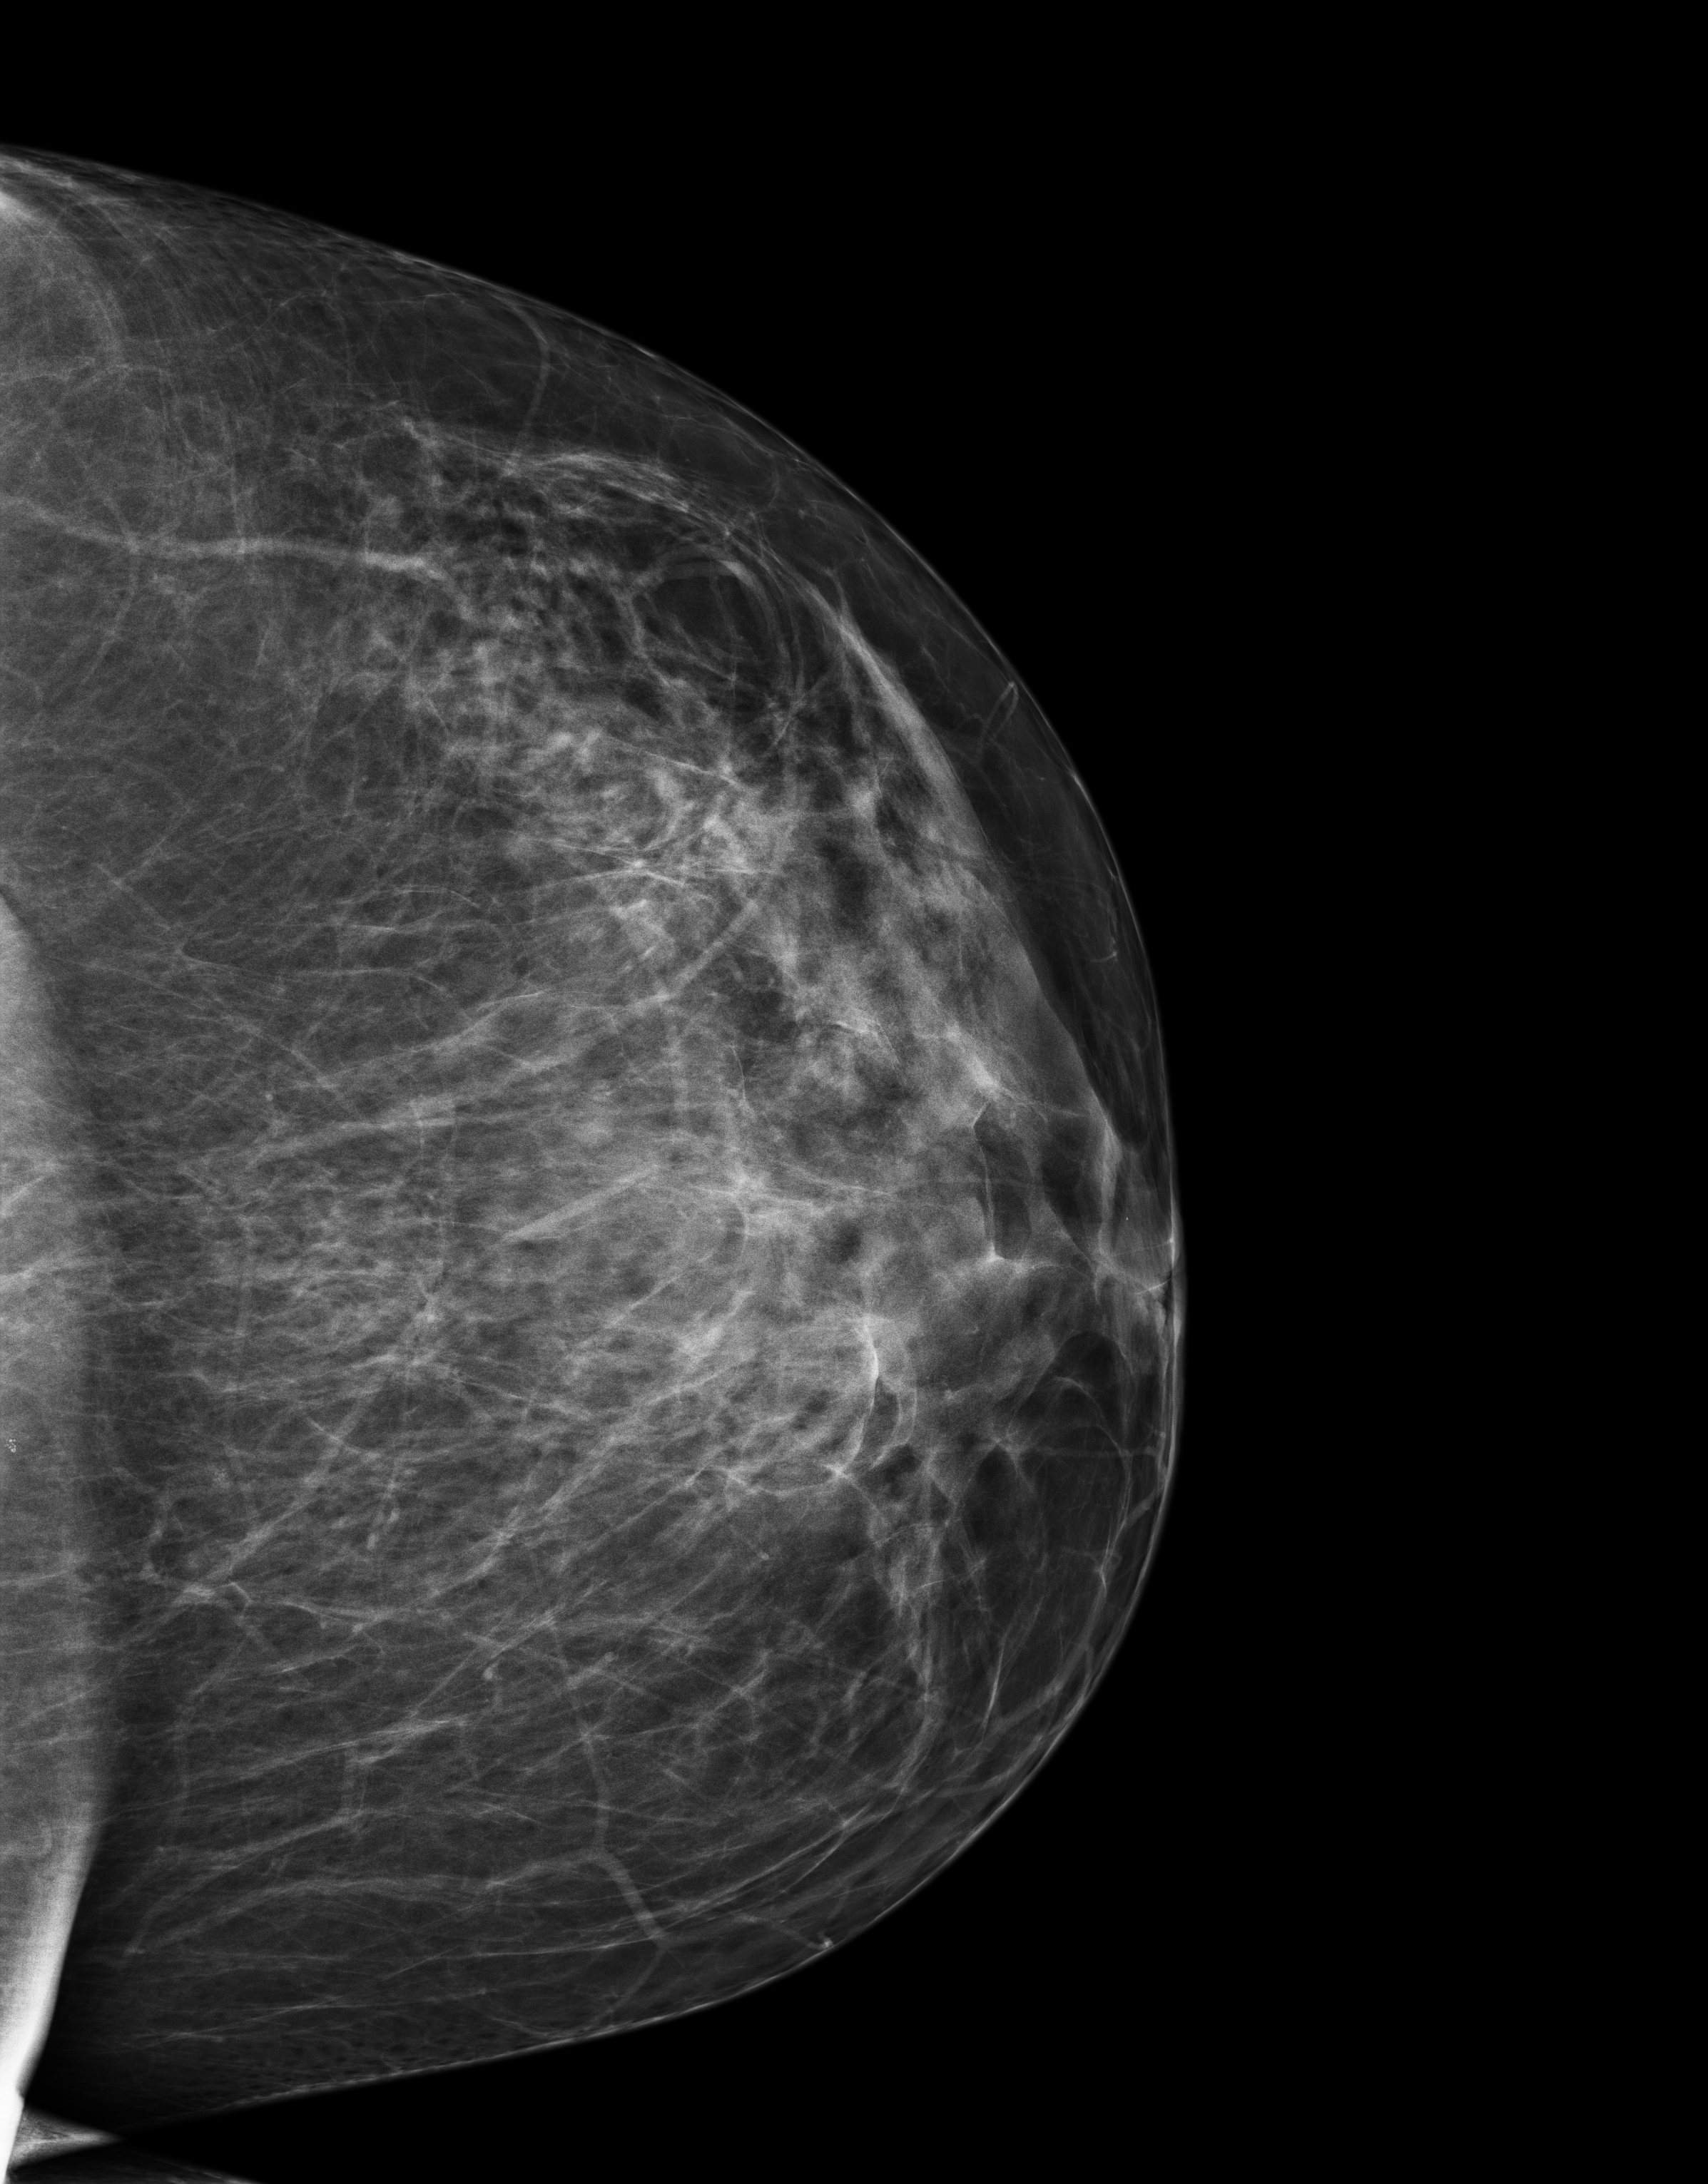
Full-field digital mammogram (FFDM); left breast; CC view; screening examination; compressed breast thickness 79 mm; system: Senographe Essential ADS_56.21.3. Female patient, age 56 years.
- breast density at the screening exam (both breasts): heterogeneously dense (BI-RADS density category c)
- final BI-RADS category for the screening round (tomosynthesis exam, both breasts): category 1
- recall: no recall after this screen